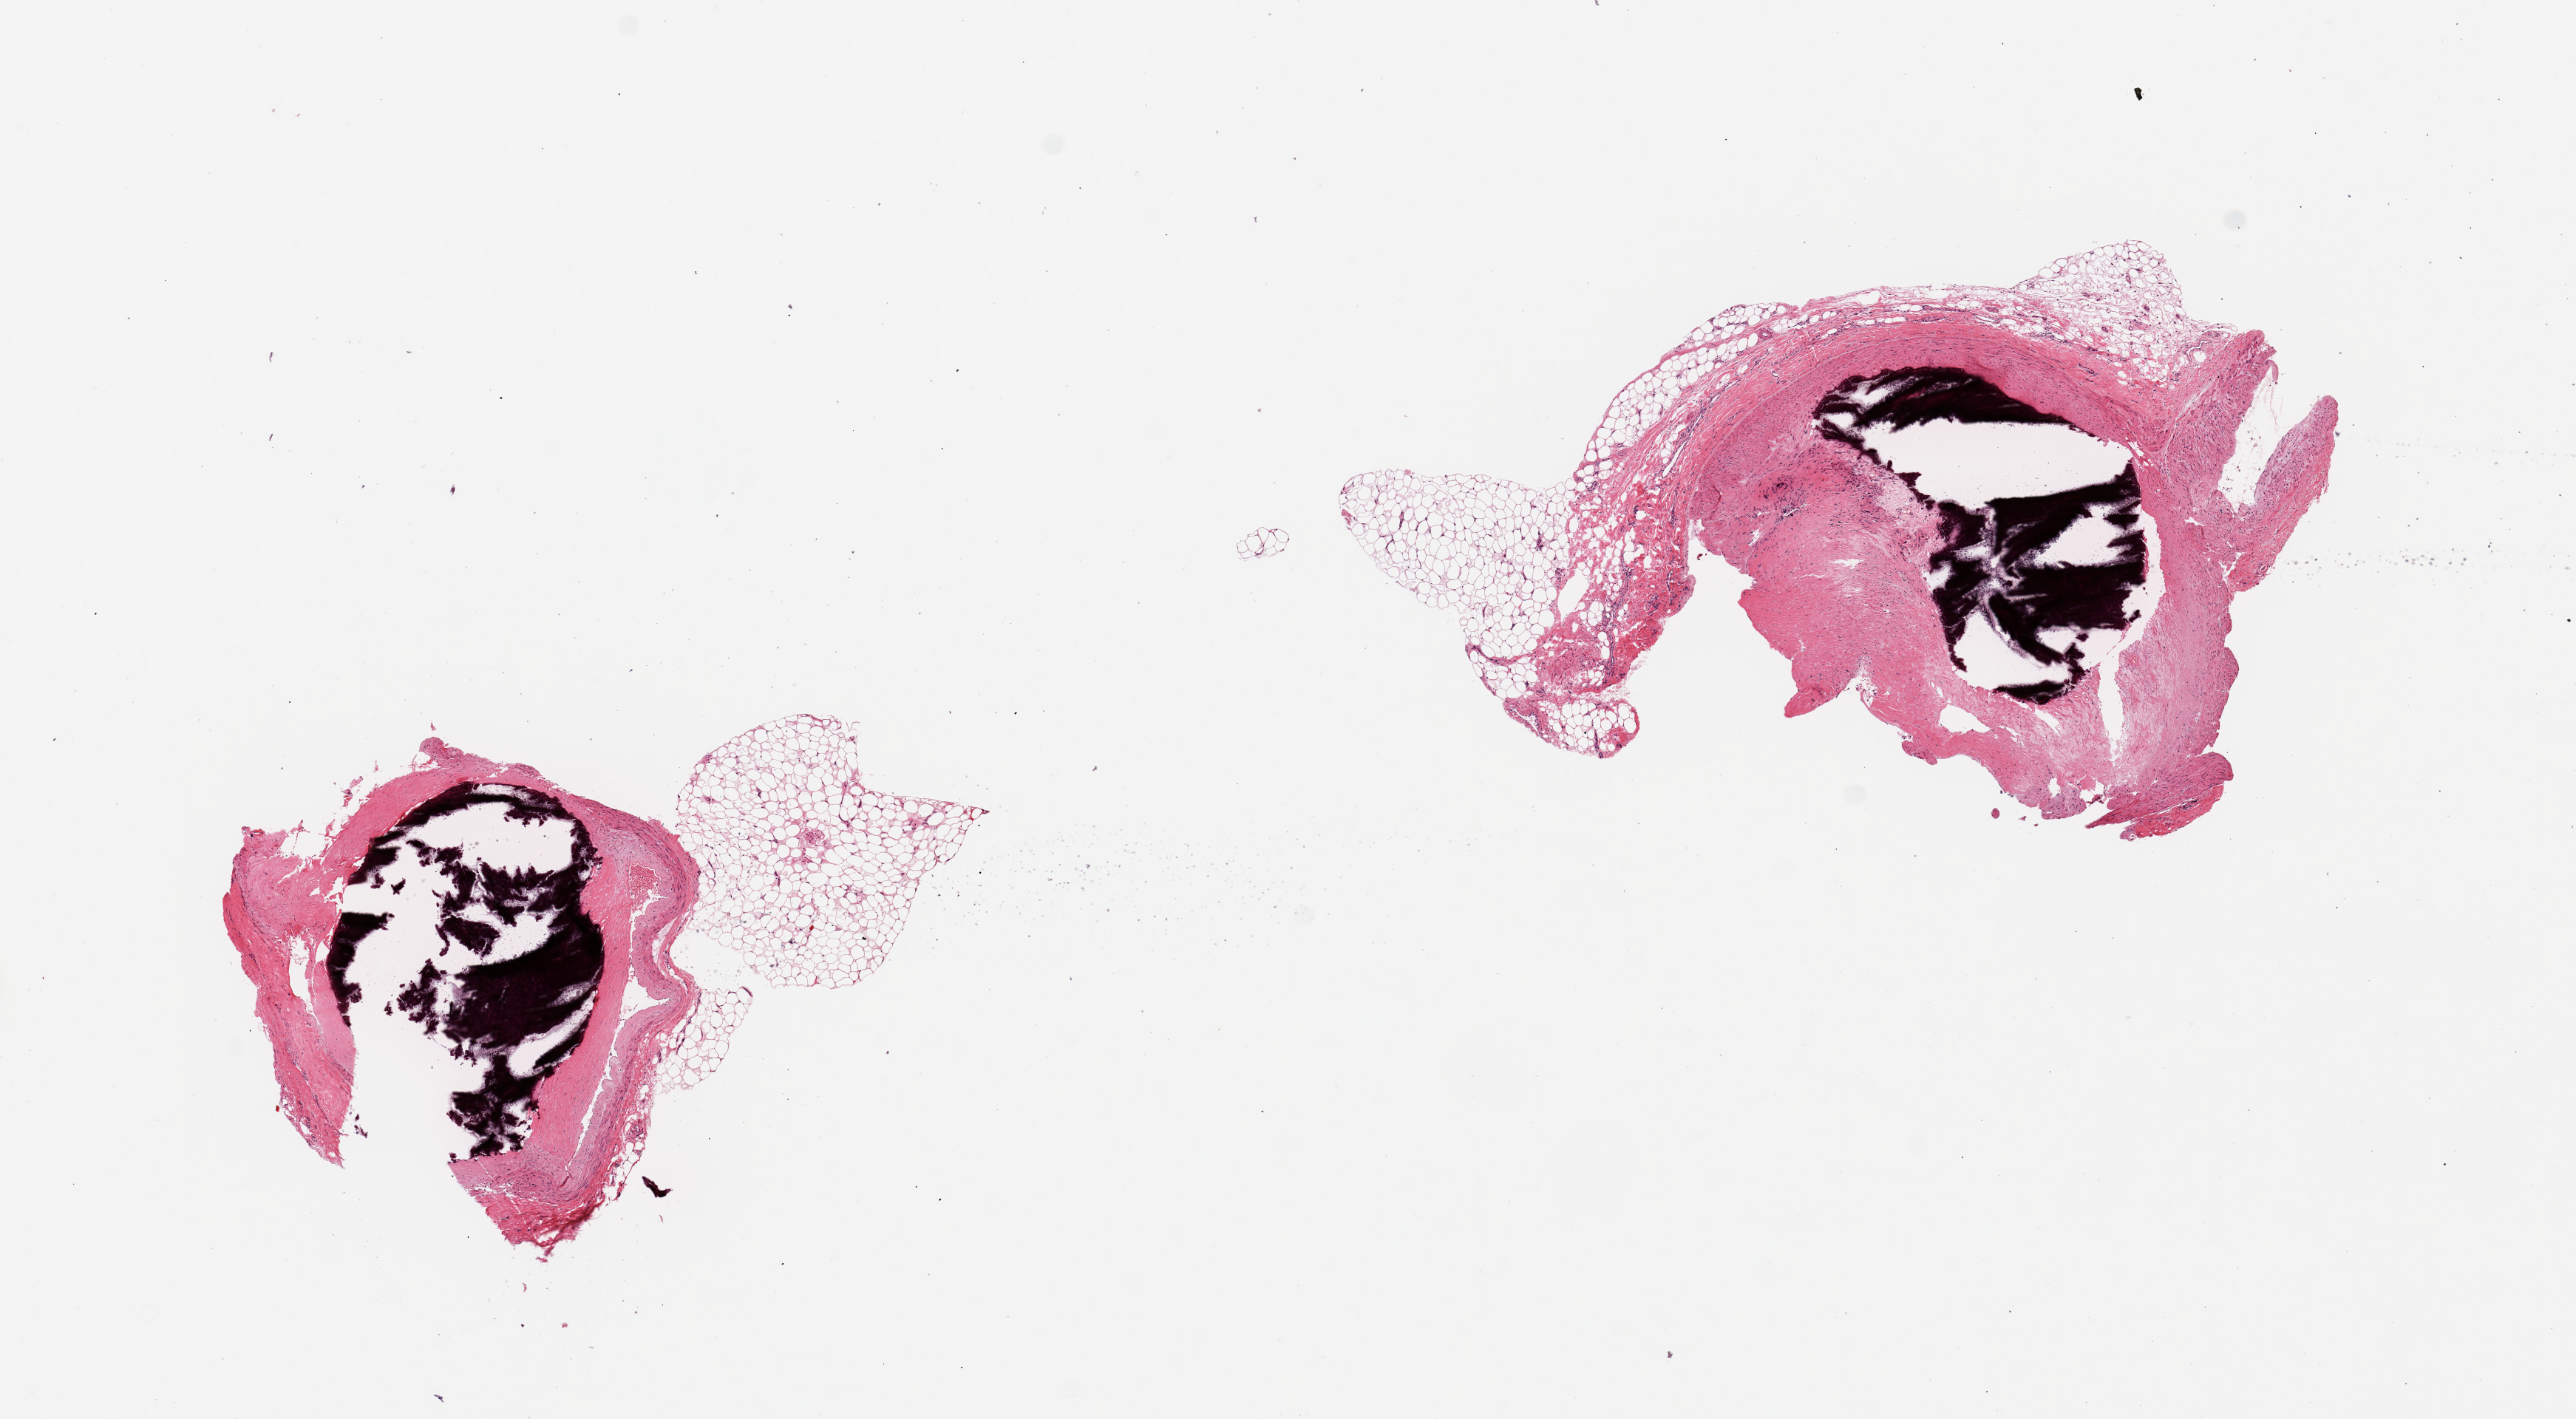
Whole-slide image, haematoxylin and eosin stain, brightfield — a low-resolution overview of the entire scanned area, about 13.8 x 7.6 mm (slide scanned at 20x); PAXgene-fixed paraffin-embedded (PFPE) section; target tissue: coronary artery; tissue donor sample. Female donor.
* review note (as recorded): 2 pieces, subtotally occlusive calcifed atherosis; Adherent fat up to ~1.5mm